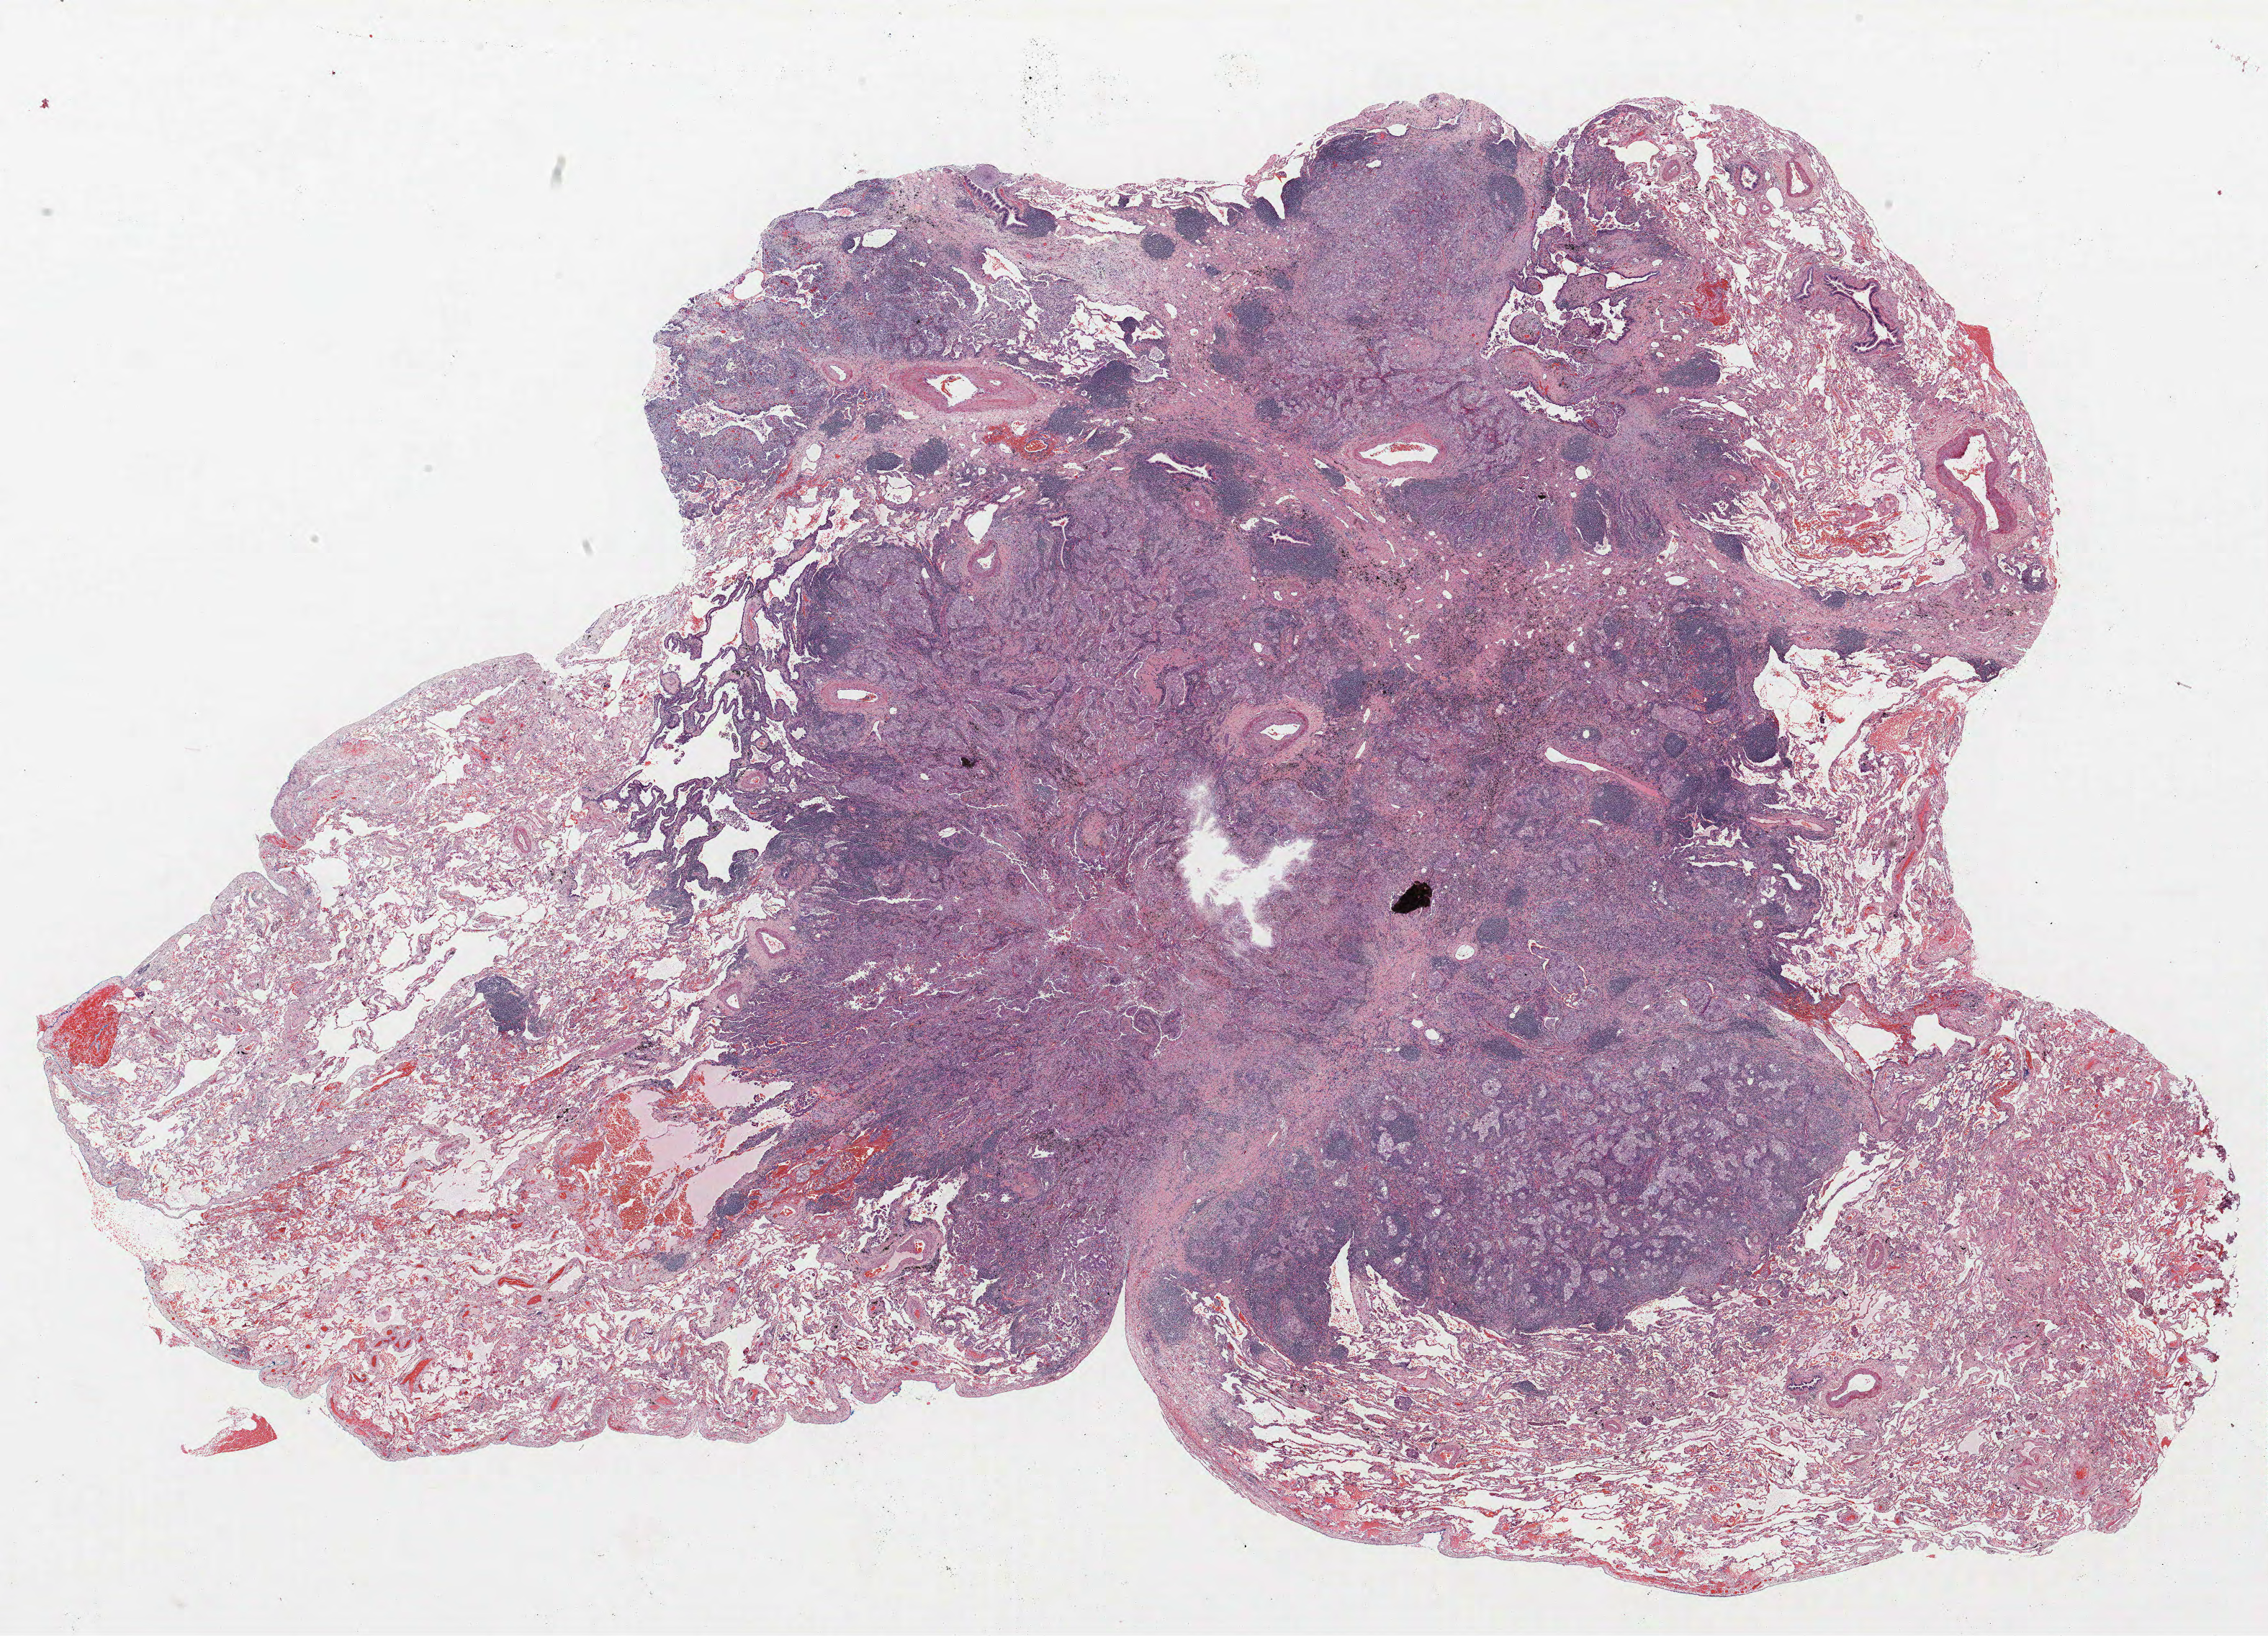
Whole-slide histology image, H&E, low-resolution overview of the scanned area, about 25.2 x 18.2 mm (acquisition: 40x scan), formalin-fixed paraffin-embedded (FFPE) section, lung tissue. Female, age 61 at enrolment. Former smoker at enrolment. Grade: poorly differentiated (G3).
* stage (AJCC 6th edition): IIIA
* primary tumour location (clinical record): right upper lobe
* tumour size (pathology): 22 mm
* ICD-O-3 topography: upper lobe of lung (C34.1)
* participant's lung-cancer diagnosis: Adenocarcinoma, NOS